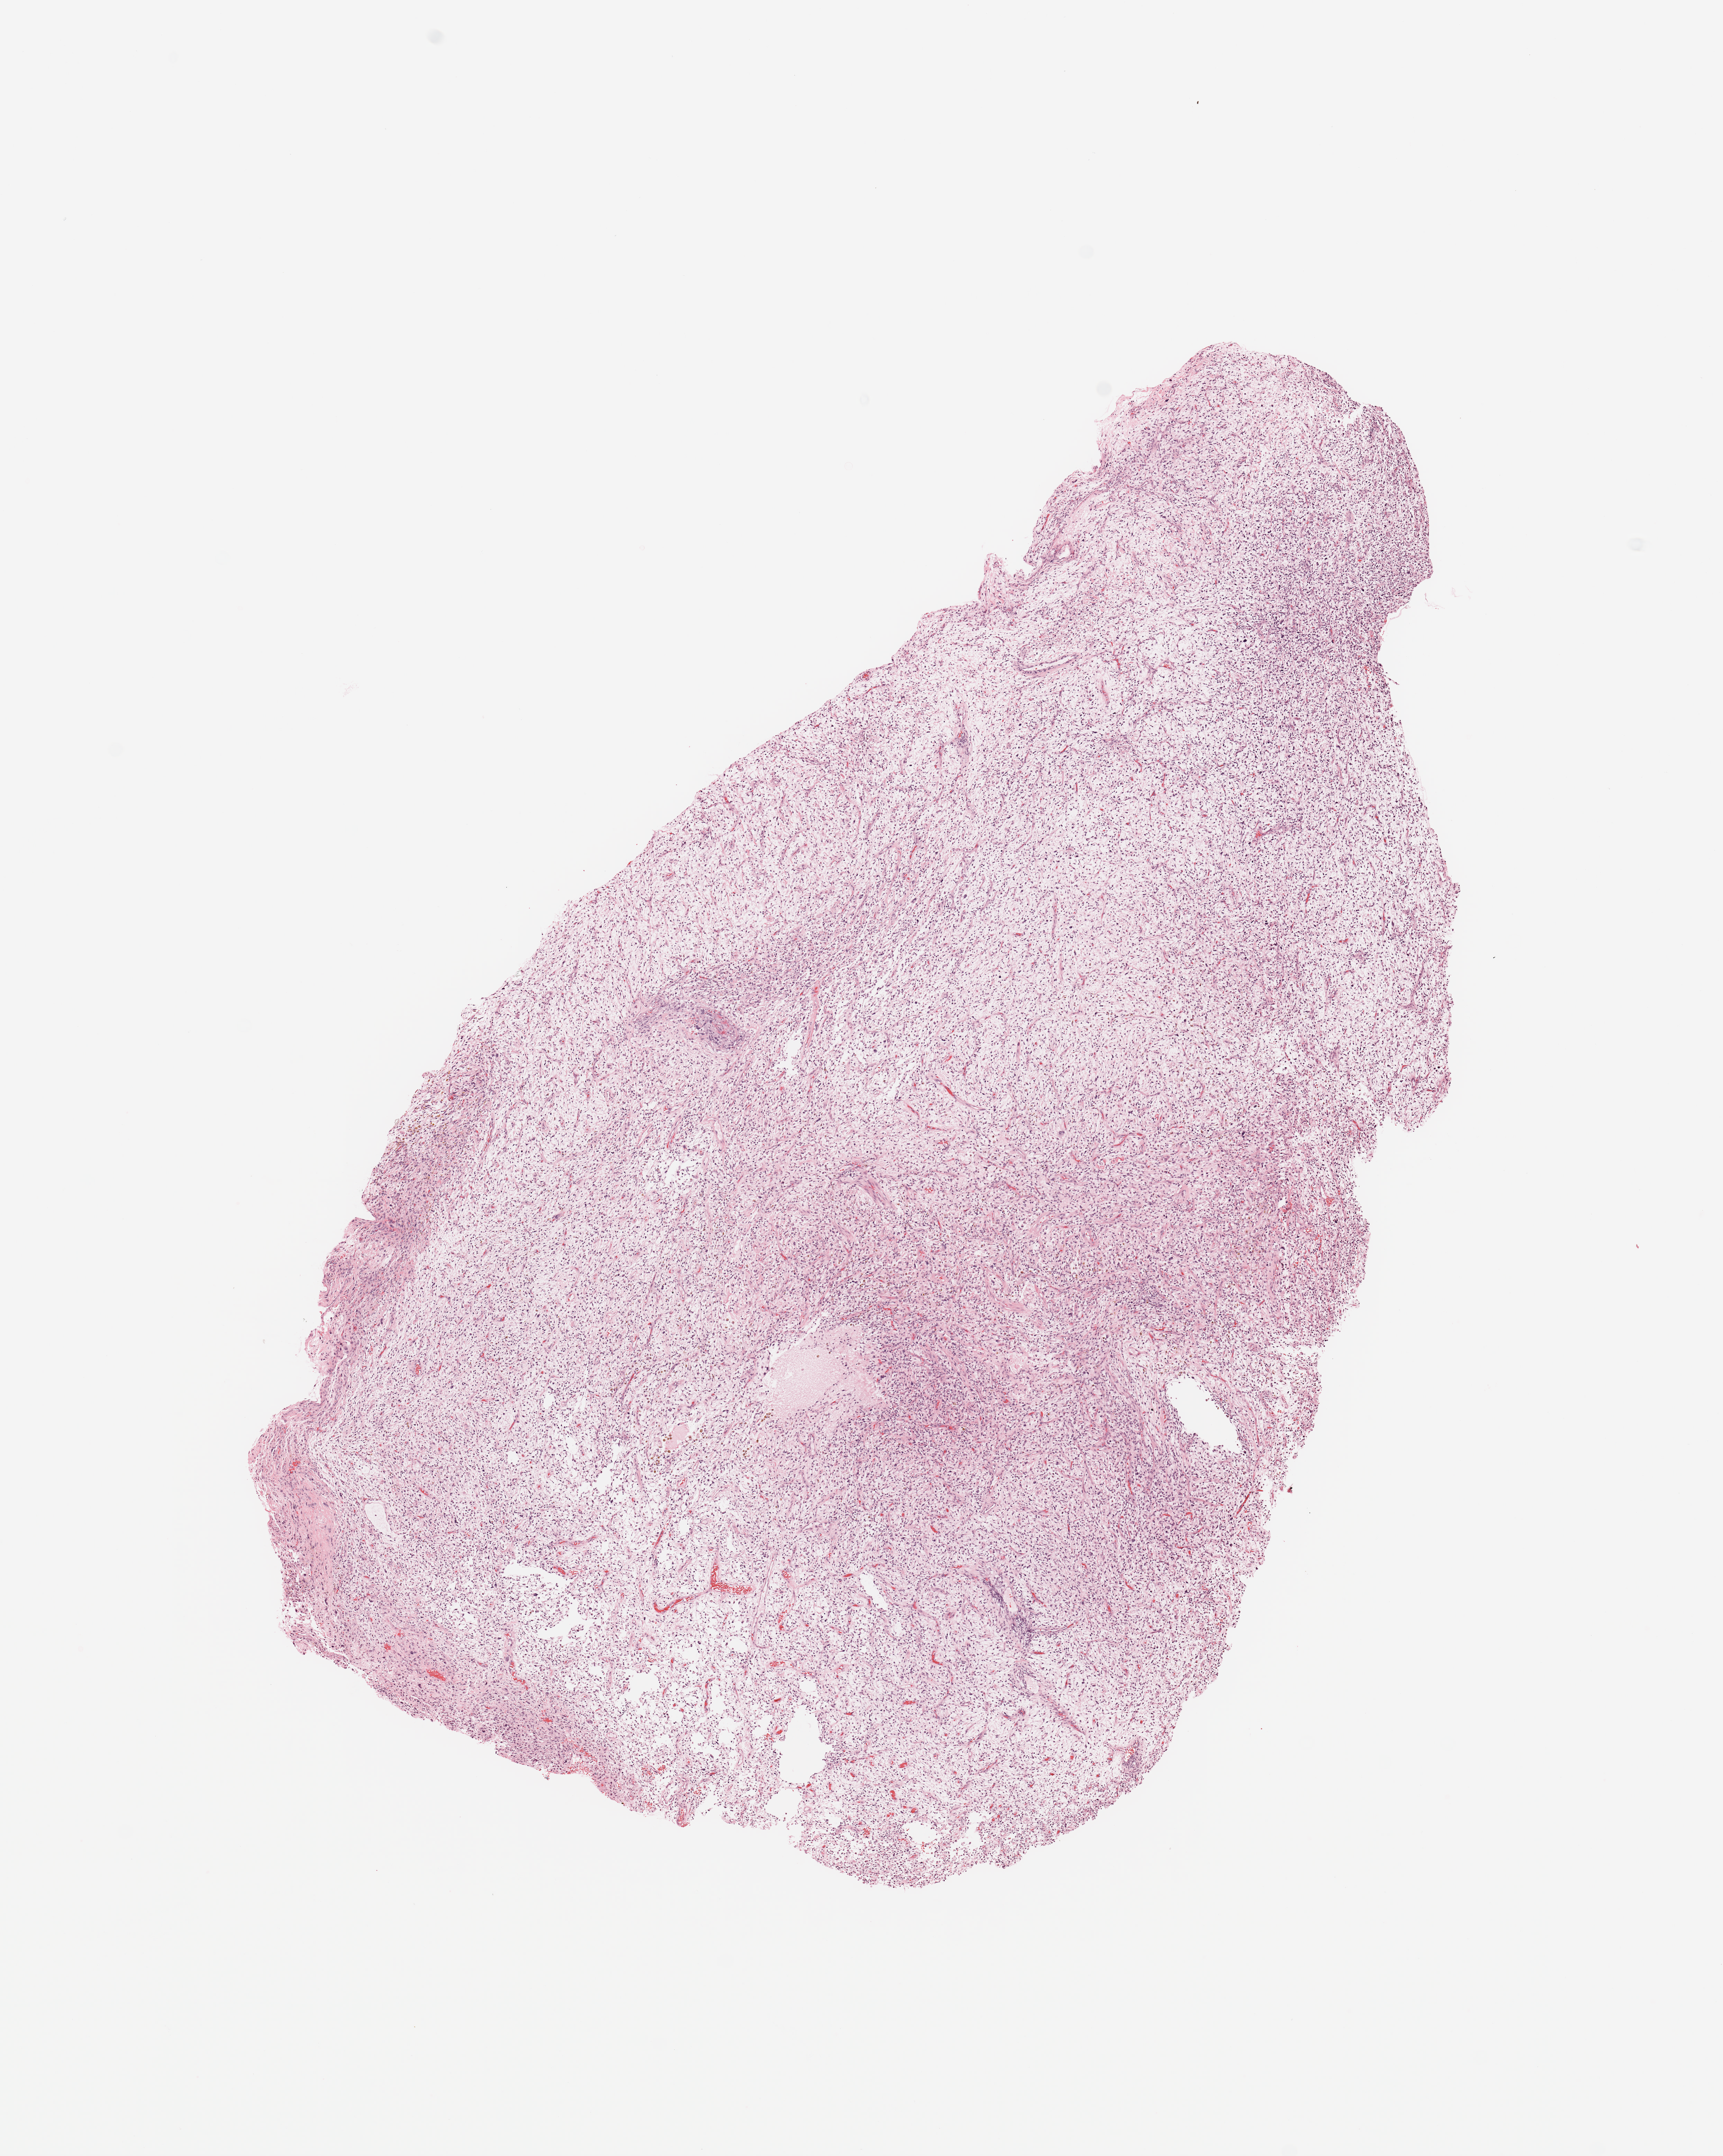
Digitized Hematoxylin and eosin (H&E) stained tissue section (whole slide) — whole scanned area (about 9.8 x 12.3 mm, slide scanned at 20x) shown as a low-resolution overview, tumour tissue sample. 52-year-old male patient.
Patient diagnosis (cohort enrolment): sarcoma (site not recorded at cohort level). Primary tumour site (as recorded): upper extremity.